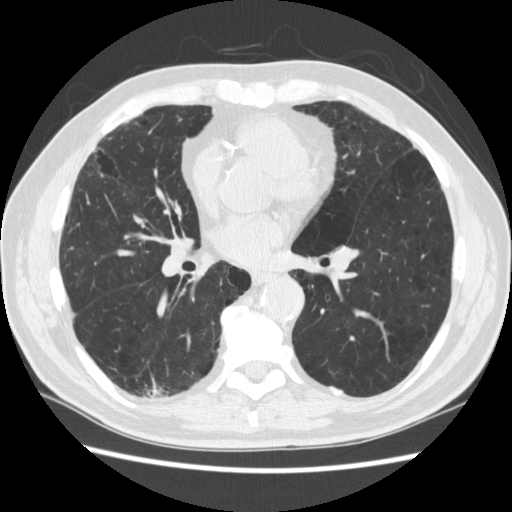
Axial slice from a low-dose chest CT screening exam, third annual screen, lung window (W 1500 / L -600 HU), 1.25 mm slice thickness, 120 kVp, slice 137 of 266 in the series, 512 × 512 image matrix, field of view 360 × 360 mm. Male, age 70 years at enrolment. Former smoker at enrolment.
Expert-annotated lung lesion, bounding box [x1, y1, x2, y2] px = [118, 361, 187, 423]. The screening reader recorded 4 non-calcified nodules or masses ≥4 mm on this exam (right lower lobe, right lower lobe, left lower lobe, left lower lobe); which of them this box marks is not recorded. Participant outcome: lung cancer diagnosed 253 days after this screen — squamous cell carcinoma, NOS, right upper lobe, poorly differentiated (G3), stage IV (AJCC 6th edition).